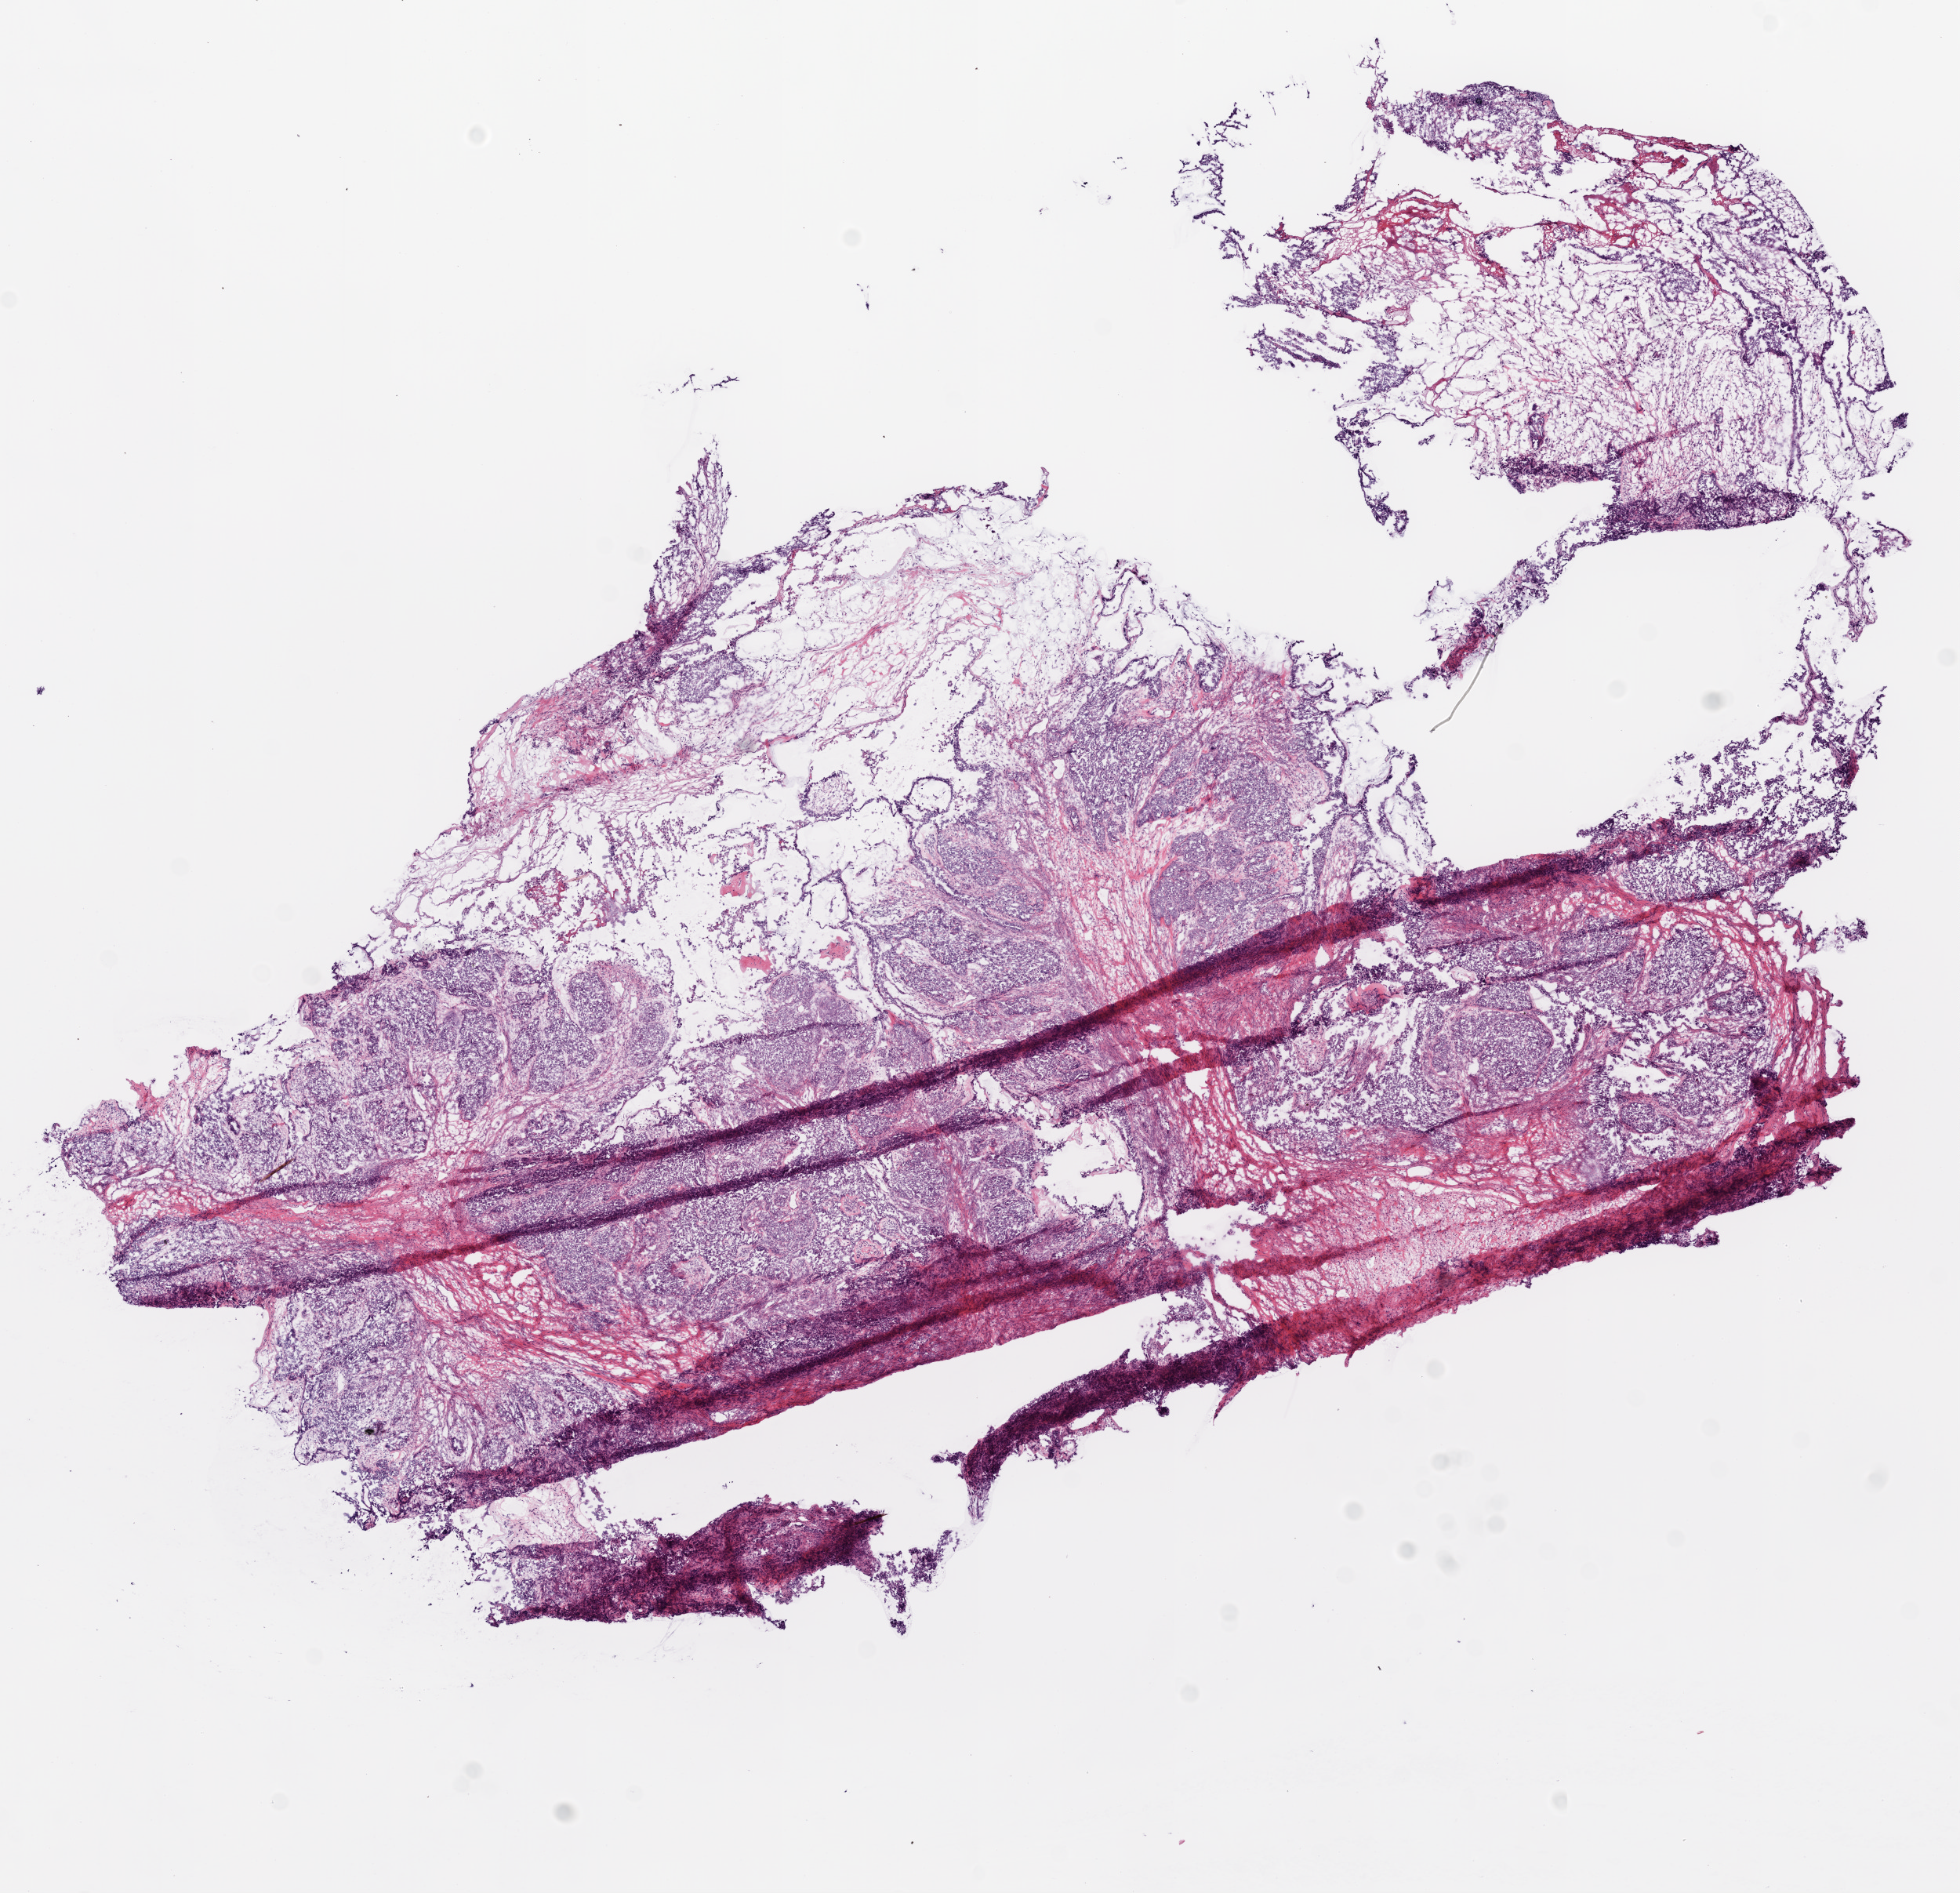
Whole-slide histology image, H&E — a low-resolution overview of the entire scanned area, about 10.0 x 9.7 mm. Frozen section from the top of the tissue portion. Ovary, primary tumour sample. Patient: female, age at initial diagnosis 66 years. Histologic grade: G3 (poorly differentiated). Pathologist review of this section (percent, as recorded): tumour cells 90%, tumour nuclei 90%, normal cells 0%, stromal cells 10%, necrosis 0%.
* diagnosis: Serous cystadenocarcinoma, NOS
* FIGO stage: IIIC